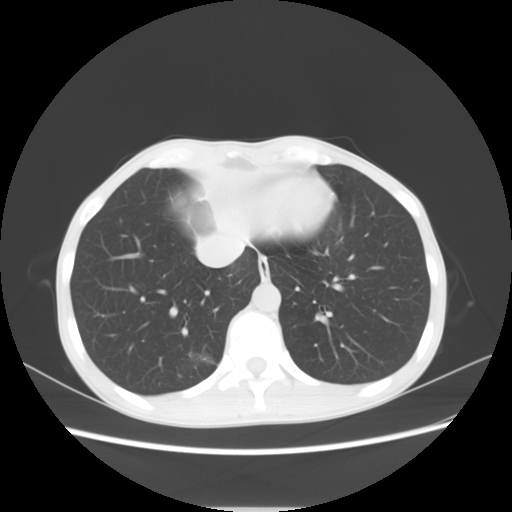
Chest CT, one axial slice; slice 21 of 69 in the series (ordered by position); lung window (W 1500 / L -600 HU); 512 × 512 image matrix. Female patient, age 51 years. Case-level facts recorded for this patient, not image findings: clinical TNM (as recorded): T1c N0 M0; histopathological grade: G2-3.
Outlined on this slice (rectangle marked by the reading radiologist):
- lung tumour (recorded histology: adenocarcinoma): box from (x=180, y=345) to (x=222, y=377) px